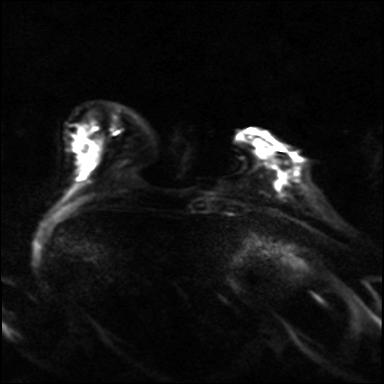
Breast MRI, one axial slice; slice 5 of 36 in the series (ordered by position); diffusion-weighted series; image 2 of 4 stored at this slice position (different b-values; order by instance number); 3 T; 384 × 384 image matrix, field of view 320 × 320 mm. Female patient.
Outlined on this slice (manually delineated by an expert):
- tumour on diffusion-weighted imaging: box from (x=282, y=174) to (x=288, y=181) px